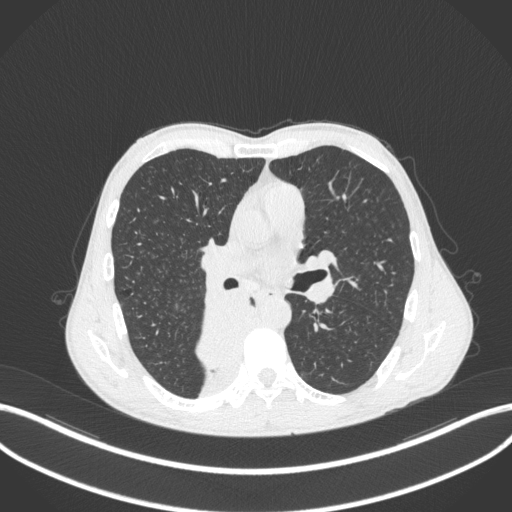
Chest CT, one axial slice; slice 213 of 371 in the series (ordered by position); reconstruction kernel B31f; 120 kVp; lung window (W 1500 / L -600 HU); 1 mm slice thickness; 512 × 512 image matrix, field of view 400 × 400 mm. Patient: male, 58 years. From the clinical record (not read from this slice): clinical TNM (as recorded): T3 N1 M1.
Annotated regions visible in this slice (bounding box drawn by a radiologist):
- lung tumour (recorded histology: squamous cell carcinoma): bounding box <187,282,260,382> (left, top, right, bottom; pixels)